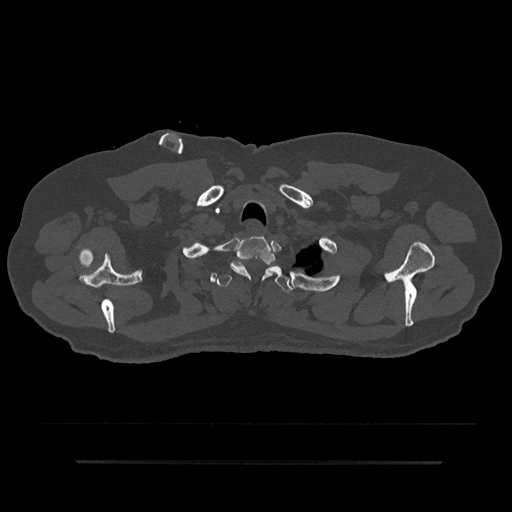
CT including the spine, one axial slice; slice 723 of 797 in the series (ordered by position); reconstruction kernel Br40s/3; 120 kVp; bone window (W 1800 / L 400 HU); 0.5 mm slice thickness; 512 × 512 image matrix, field of view 464 × 464 mm. Male patient, age 59 years. From the clinical record (not read from this slice): primary cancer: bile ducts; vertebrae with lytic lesions (as recorded): T10.
Structures marked on this image (semi-automatic segmentation, software-assisted and operator-edited):
- T1 vertebra: bounding box (x1, y1, x2, y2) in pixels: (230, 236, 276, 279)
- T2 vertebra: (216, 265, 292, 293)